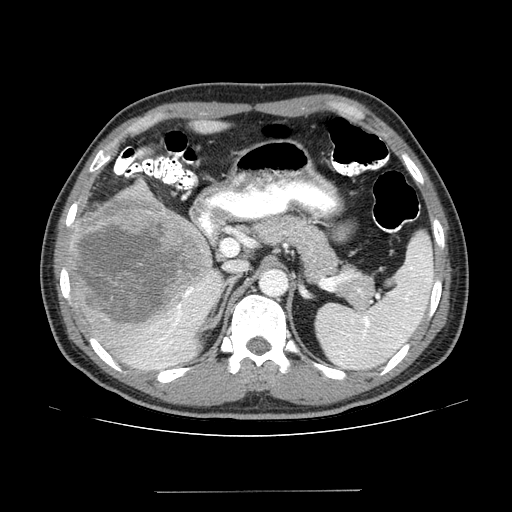
Contrast-enhanced abdominal CT (liver protocol), one axial slice; position 84 of 131 along the scan axis; reconstruction kernel STANDARD; 100 kVp; one of 2 acquisitions stored at this slice position; soft-tissue window (W 400 / L 40 HU); 2.5 mm slice thickness; 512 × 512 image matrix, field of view 380 × 380 mm. Case-level facts recorded for this patient, not image findings: diagnosis: hepatocellular carcinoma (patient treated with transarterial chemoembolisation; whether this scan precedes or follows treatment is not stated here); TNM stage (as recorded): Stage-I; Child-Pugh class: A; tumour differentiation: poorly differentiated; tumour size: 10.3 cm.
Outlined on this slice (semi-automatically segmented with operator editing):
- liver parenchyma outside the tumour (the mass and vessels are separate outlines, so this box may not span the whole liver): bounding box (x1, y1, x2, y2) in pixels: (66, 180, 224, 370)
- mass: (67, 187, 212, 329)
- liver vessels: (139, 280, 209, 369)